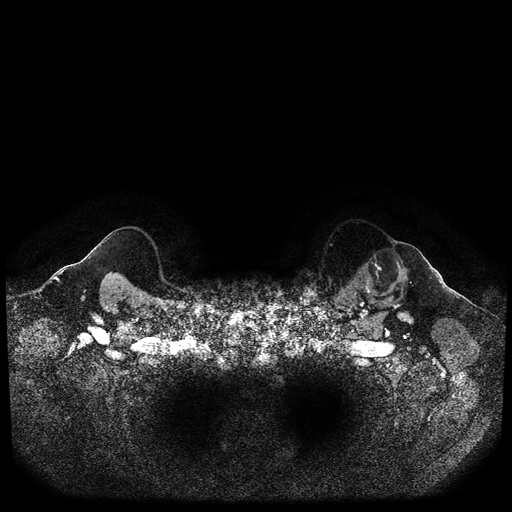
Breast MRI (dynamic contrast-enhanced, multi-phase), one axial slice. Slice 95 of 116 in the series (ordered by position). Dynamic contrast-enhanced series, time point 2 of 5 at this slice position (early post-contrast). 1.5 T. TE 2.6 ms, TR 5.3 ms. 512 × 512 image matrix, field of view 350 × 350 mm. Patient: female, 64 years.
Outlined on this slice (semi-automatic segmentation, software-assisted and operator-edited):
- breast lesion (labelled 'tumour' in the annotation; benign lesions carry a separate 'benign' label): box from (x=357, y=248) to (x=408, y=305) px